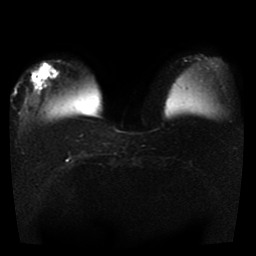
Breast MRI, one axial slice; slice 11 of 41 in the series (ordered by position); diffusion-weighted series; image 2 of 4 stored at this slice position (different b-values; order by instance number); 1.5 T; 5 mm slice thickness; 256 × 256 image matrix. Female patient.
Structures marked on this image (outlined manually by an expert reader):
- tumour on diffusion-weighted imaging: bounding box <31,69,47,87> (left, top, right, bottom; pixels)